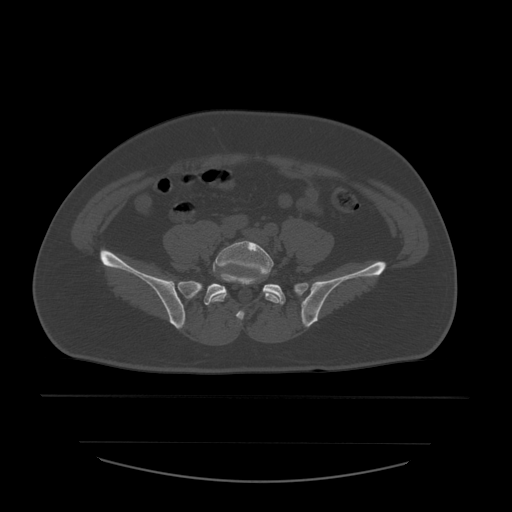
CT including the spine, one axial slice; position 110 of 532 along the scan axis; reconstruction kernel STANDARD; 120 kVp; bone window (W 1800 / L 400 HU); 1.25 mm slice thickness; 512 × 512 image matrix. Patient age 44 years. From the clinical record (not read from this slice): primary cancer: soft tissue sarcoma.
Structures marked on this image (semi-automatically segmented with operator editing):
- L5 vertebra: bounding box (x1, y1, x2, y2) in pixels: (212, 241, 280, 304)